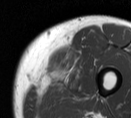
MRI of an extremity soft-tissue mass, one axial slice. Slice 13 of 55 in the series (ordered by position). MR volume resampled by the dataset authors to the PET/CT grid (not the native acquisition matrix). 3.27 mm slice thickness. 131 × 118 image matrix. Male patient. Case-level facts recorded for this patient, not image findings: histological type: pleiomorphic liposarcoma; grade: high; site of the primary tumour: left thigh.
Structures marked on this image (expert contour drawn on MRI and transferred to this co-registered scan by the dataset authors):
- gross tumour volume including surrounding oedema: bounding box <41,55,88,97> (left, top, right, bottom; pixels)
- gross tumour volume (mass): <41,55,63,79>